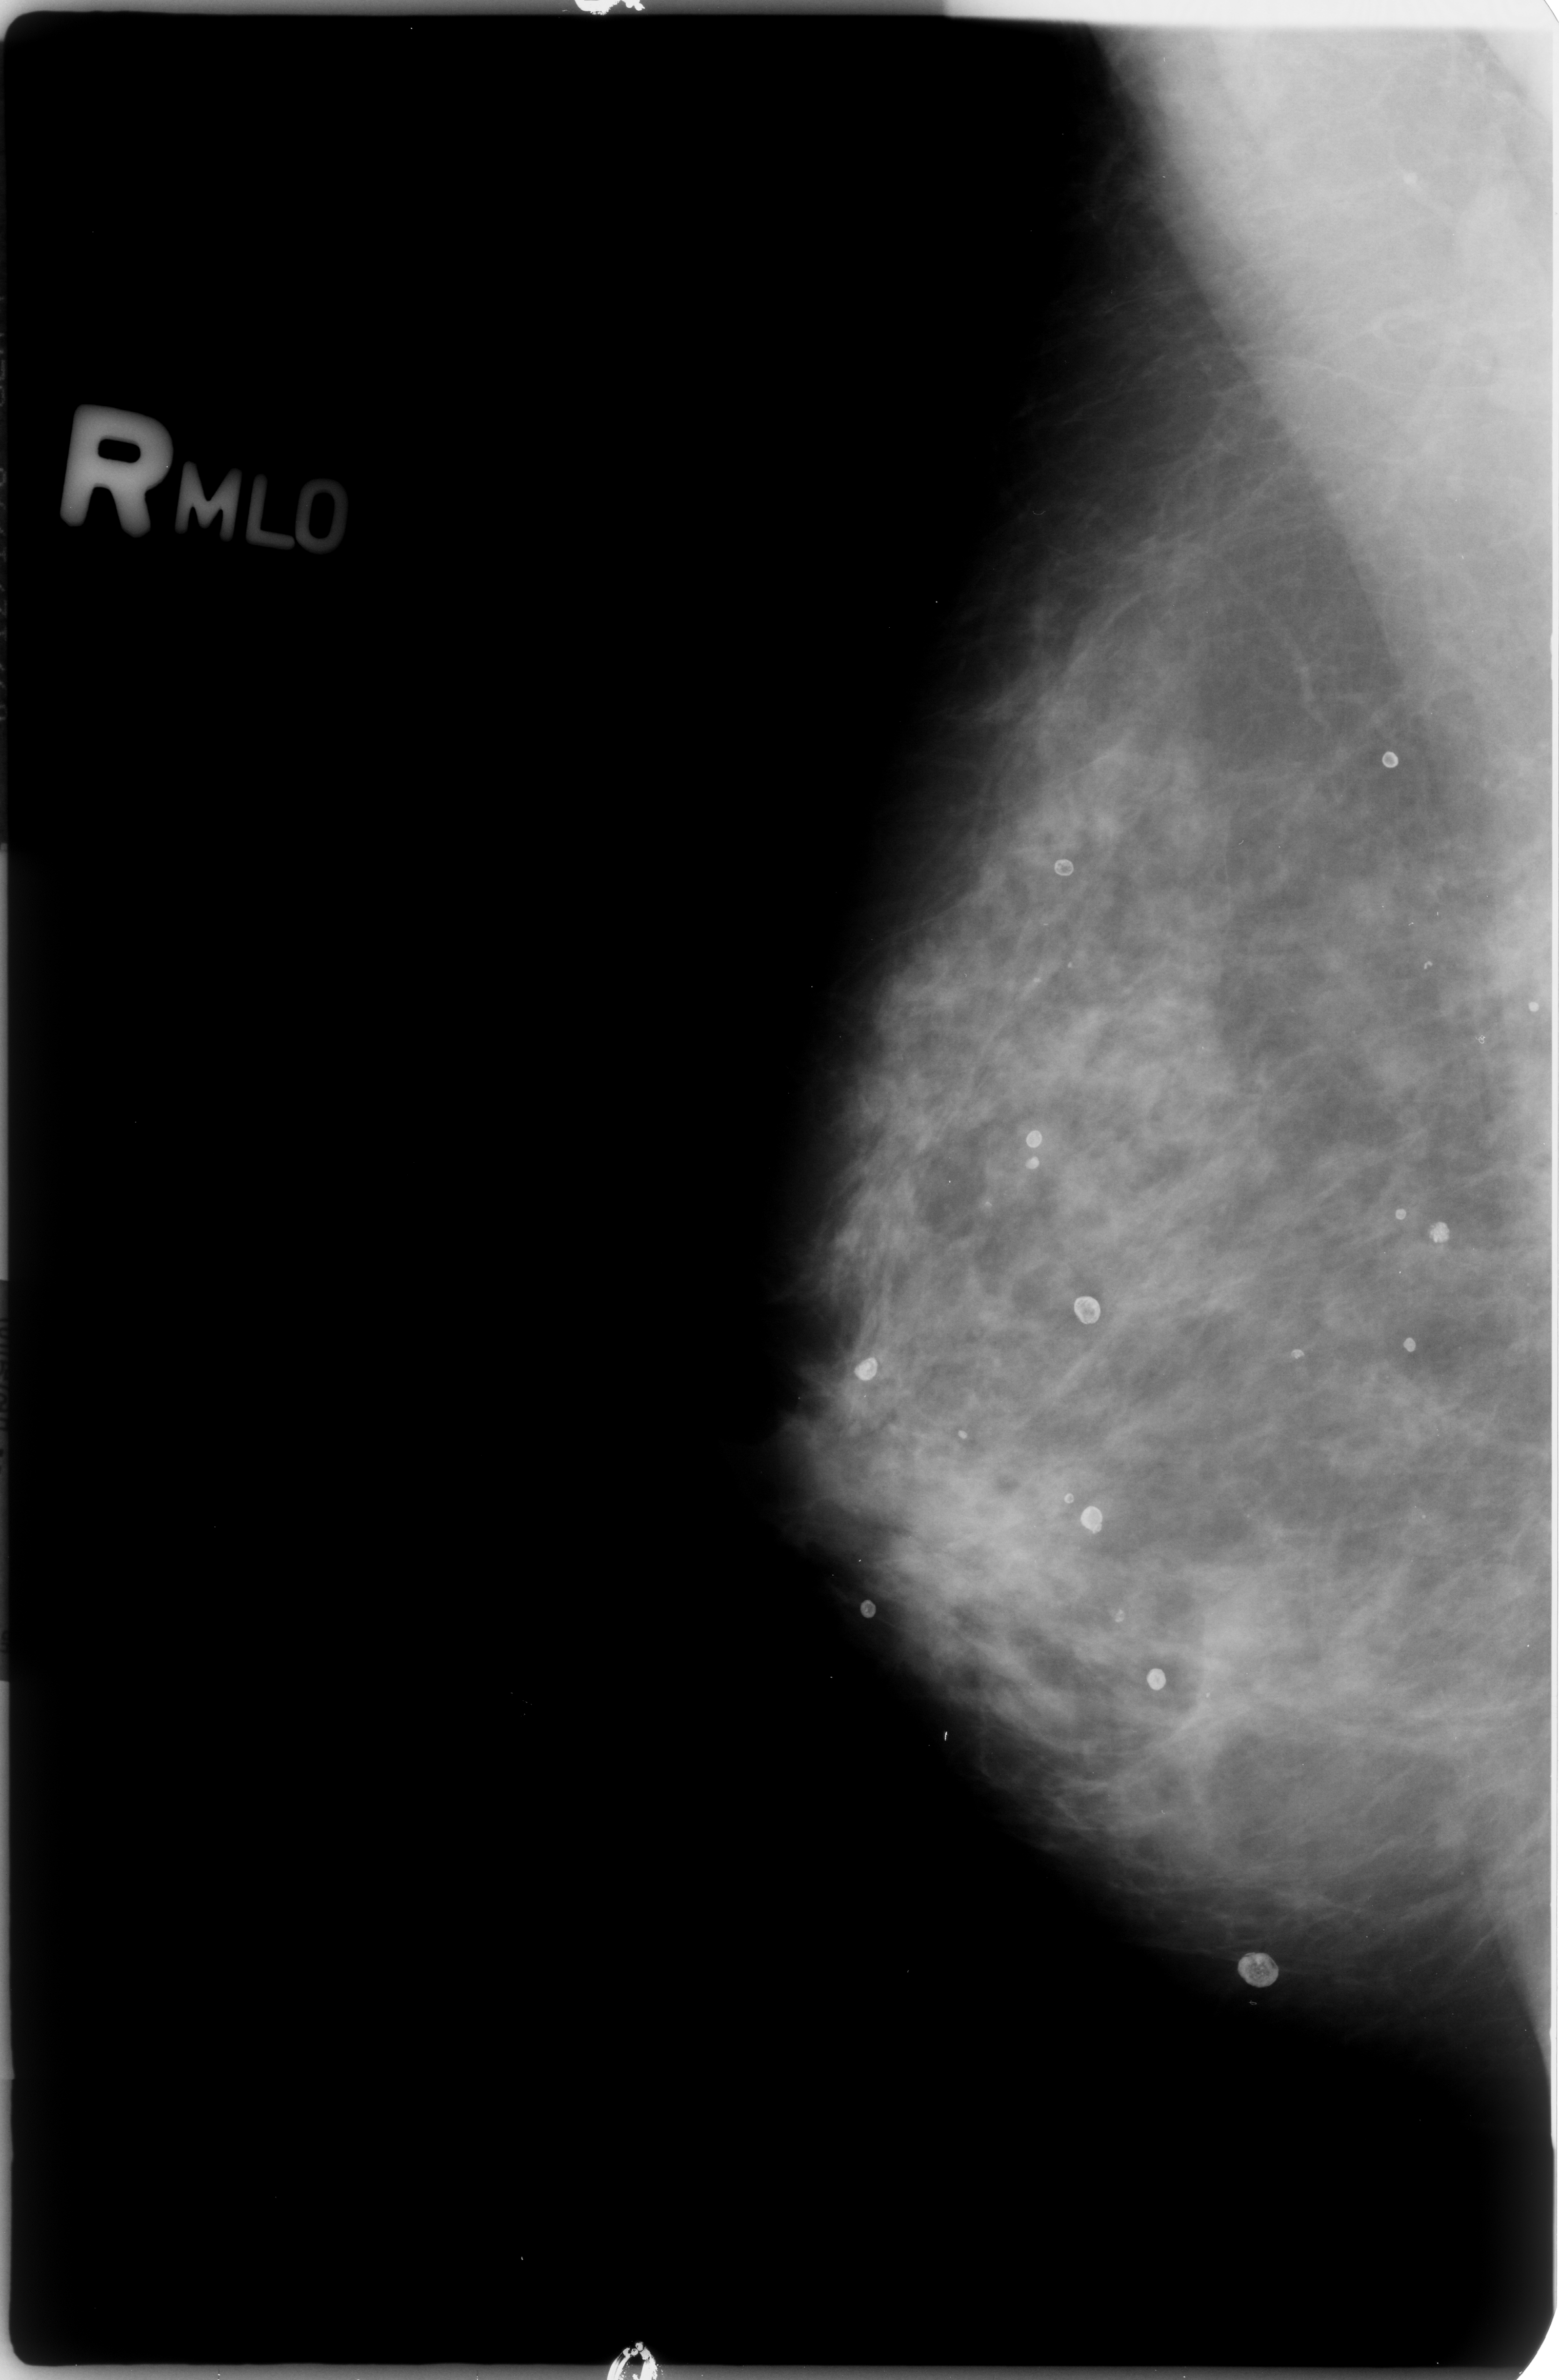
Digitized screen-film mammogram, right breast, MLO view, BI-RADS breast density category 3 (scale 1–4).
- Abnormality record for this image: Finding 1 of 7: calcifications, morphology round and regular / eggshell; BI-RADS assessment category 2; benign without callback (not worked up further).
- Finding 2 of 7: calcifications, morphology round and regular / eggshell; BI-RADS assessment category 2; subtlety rating 3 on a 1 (subtle) to 5 (obvious) scale; benign without callback (not worked up further).
- Finding 3 of 7: calcifications, morphology round and regular / eggshell; BI-RADS assessment category 2; subtlety rating 3 on a 1 (subtle) to 5 (obvious) scale; benign without callback (not worked up further).
- Finding 4 of 7: calcifications, morphology round and regular / eggshell; BI-RADS assessment category 2; benign without callback (not worked up further).
- Finding 5 of 7: calcifications, morphology round and regular / eggshell; BI-RADS assessment category 2; benign without callback (not worked up further).
- Finding 6 of 7: calcifications, morphology round and regular / eggshell; BI-RADS assessment category 2; benign; no additional work-up was recommended (benign without callback).
- Finding 7 of 7: calcifications, morphology round and regular / eggshell; BI-RADS assessment category 2; benign without callback (not worked up further).